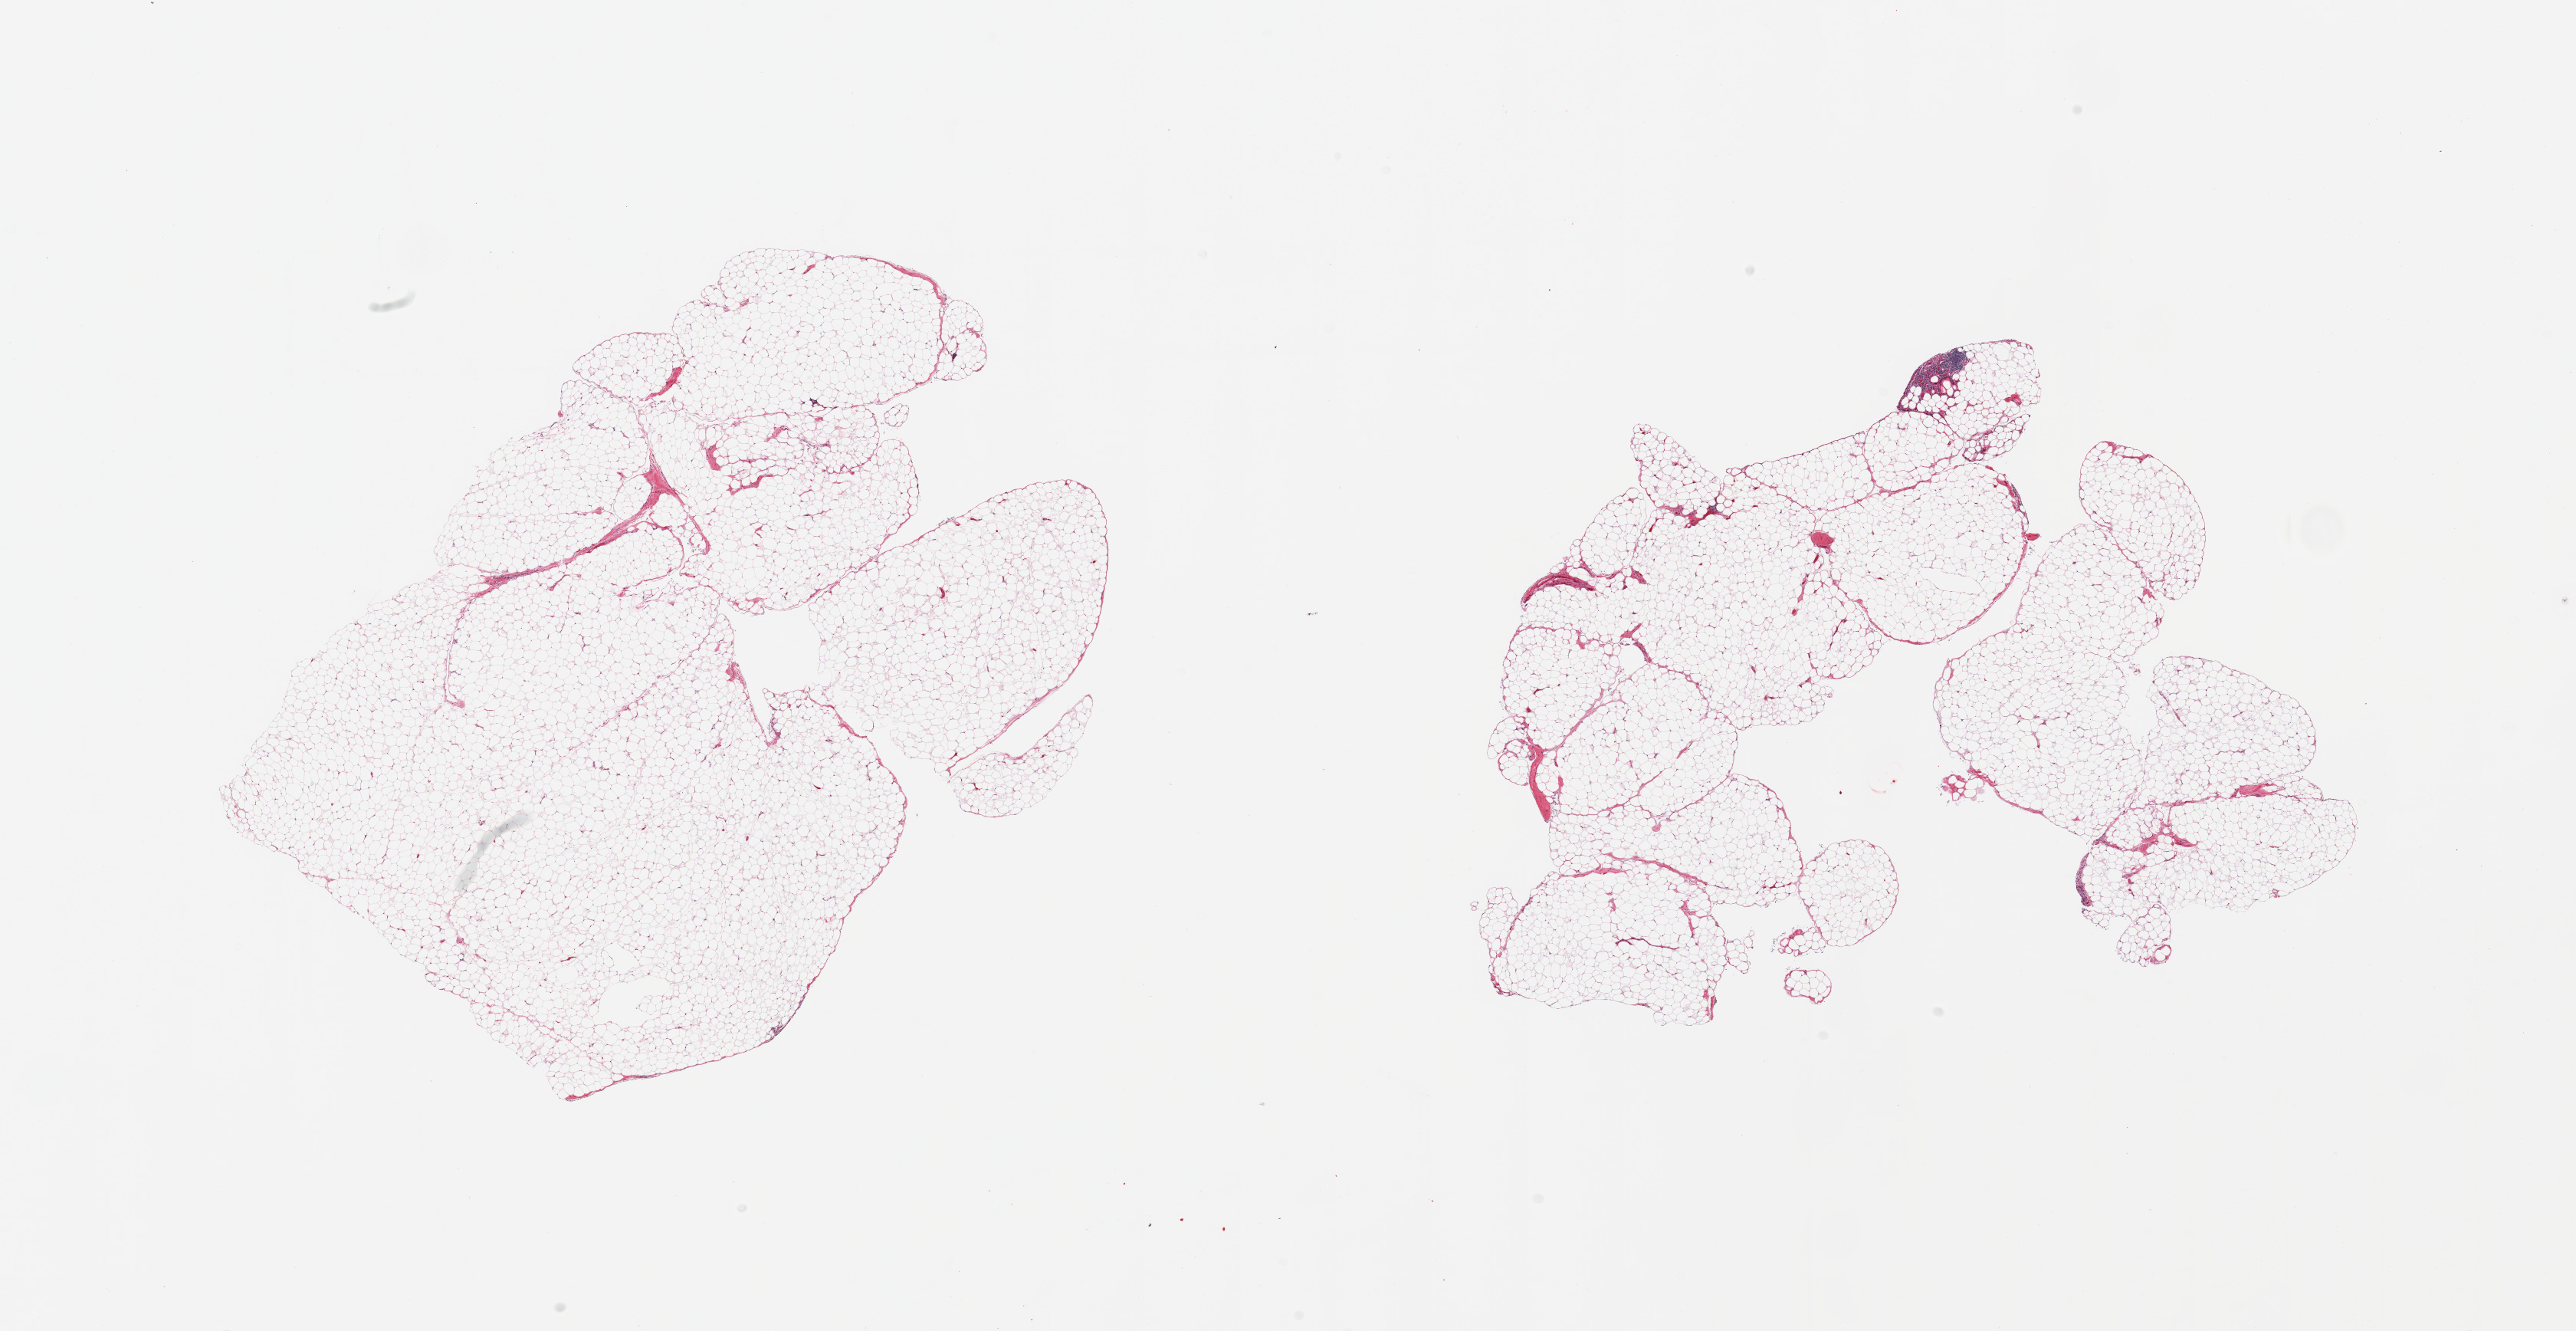
Whole-slide image, hematoxylin and eosin (H&E) stain — a low-resolution overview of the entire scanned area, about 26.6 x 13.7 mm, PAXgene-fixed, paraffin-embedded tissue, section of omentum (target tissue), tissue donor sample. Donor: male.
Review note (as recorded): 2 pieces minute lymphoid aggregate (~0.5mm).